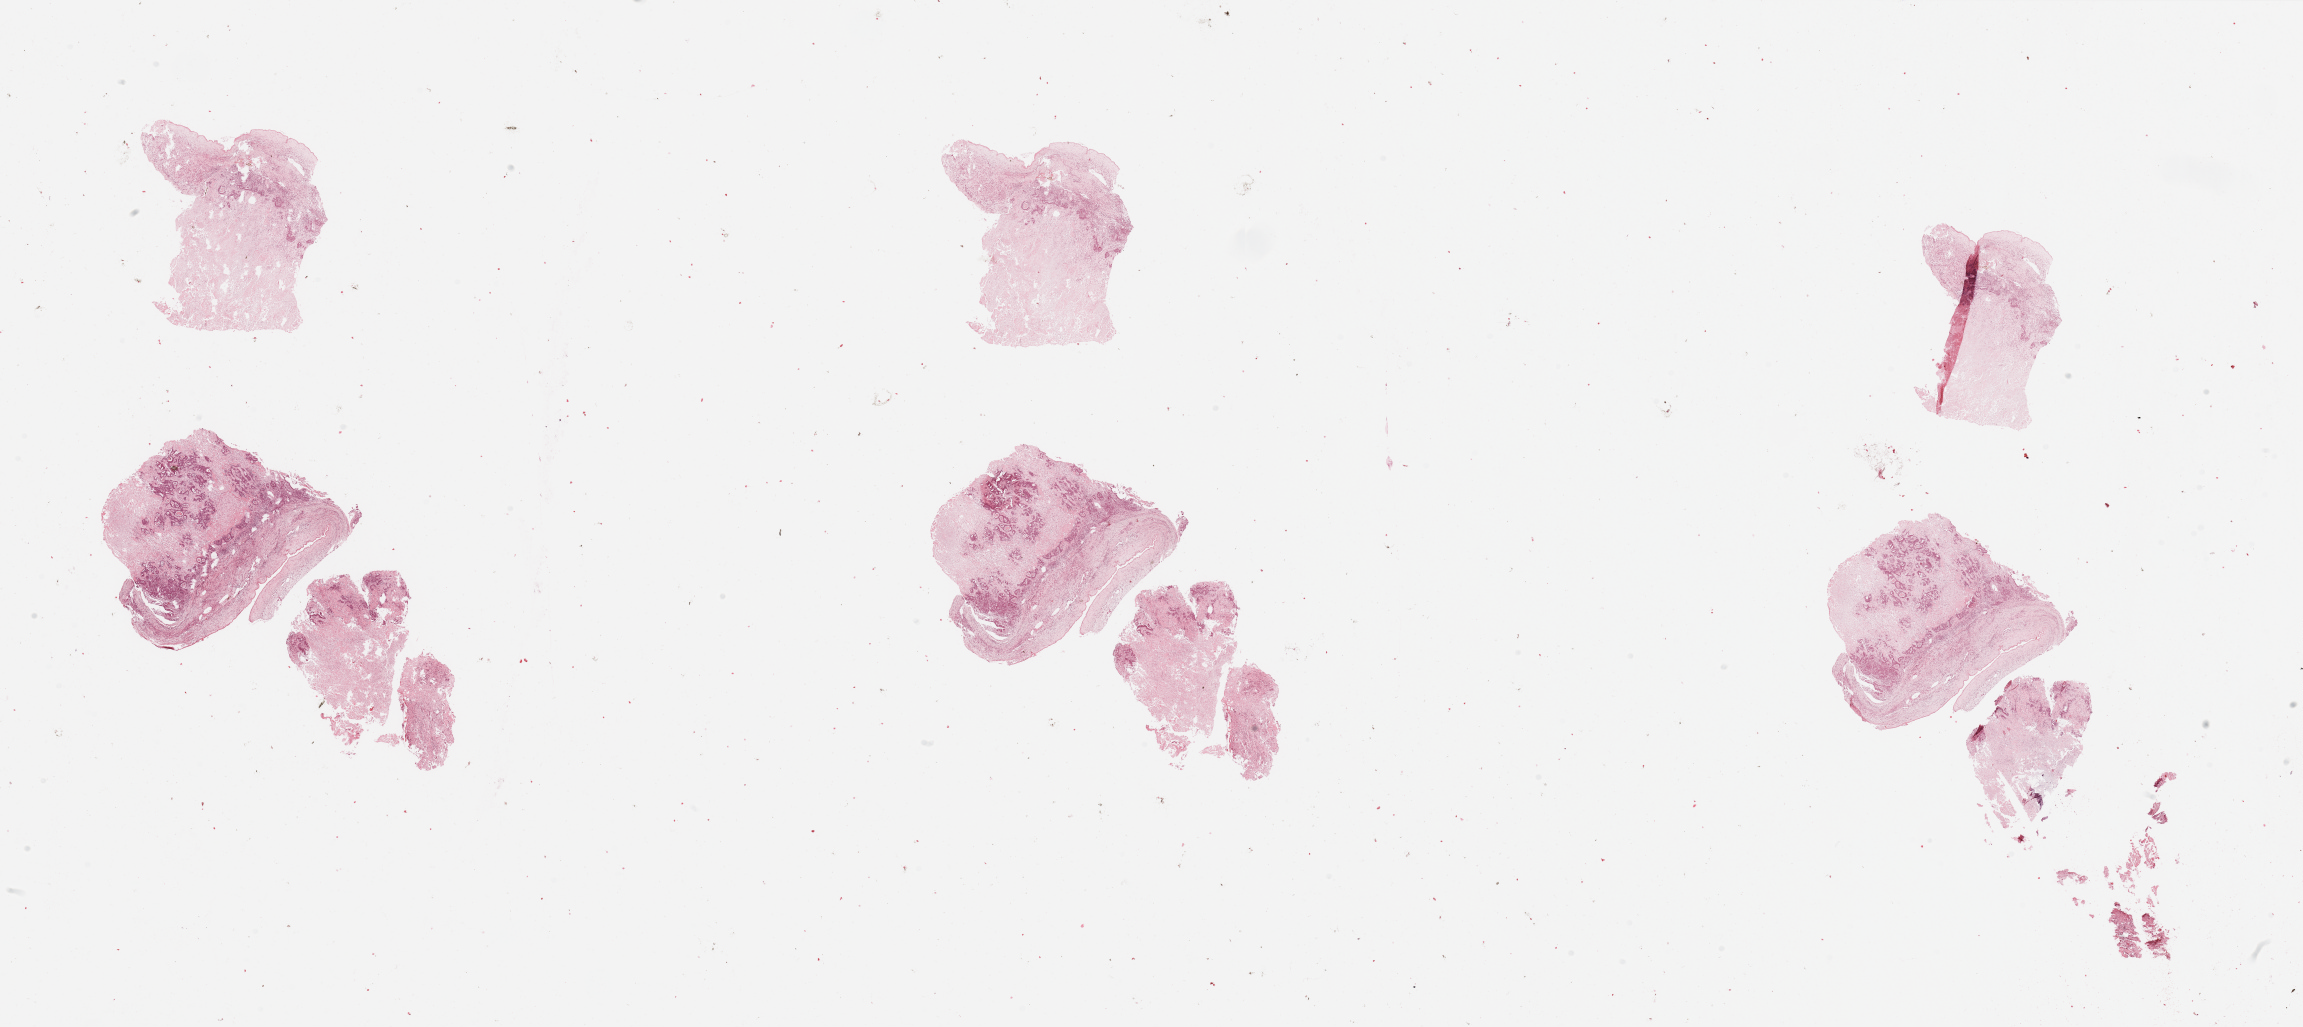
Digitized Hematoxylin and eosin (H&E) stained tissue section (whole slide), low-resolution overview of the scanned area, about 36.4 x 16.2 mm, tumour tissue sample, sampled site: pancreas. 68-year-old female patient. Histologic grade: G2 (moderately differentiated). Slide review estimates, as recorded: tumour nuclei 40%, necrosis 20%.
* diagnosis: Infiltrating duct carcinoma, NOS
* primary tumour site (as recorded): head